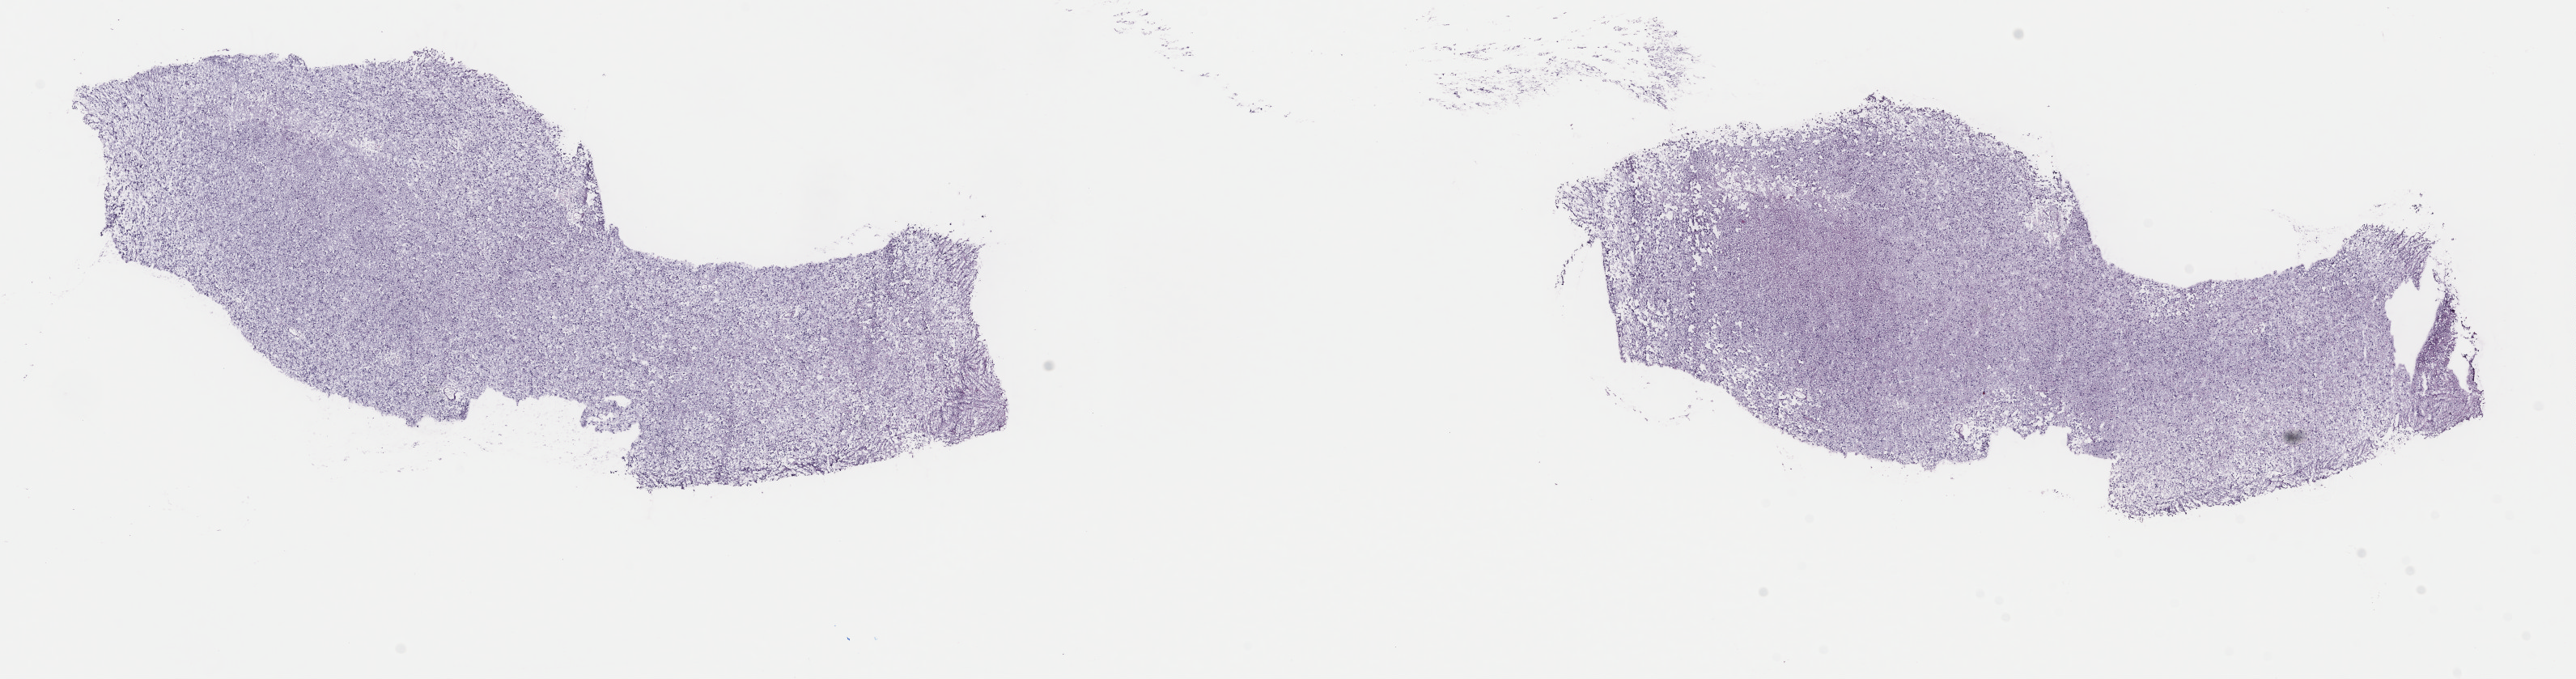
Hematoxylin and eosin (H&E) stained whole-slide image — a low-resolution overview of the entire scanned area, about 25.1 x 6.6 mm. Frozen section from the top of the tissue portion. Sample: primary tumour, brain. Male, age 38 years at initial diagnosis. Histologic grade: G2 (moderately differentiated). Composition of this section per pathologist review: tumour cells 60%, tumour nuclei 80%, normal cells 10%, stromal cells 30%, necrosis 0%. Infiltration values recorded for this section: lymphocyte infiltration 0%, monocyte infiltration 0%, neutrophil infiltration 0%.
Histologic diagnosis: Mixed glioma (cerebrum).